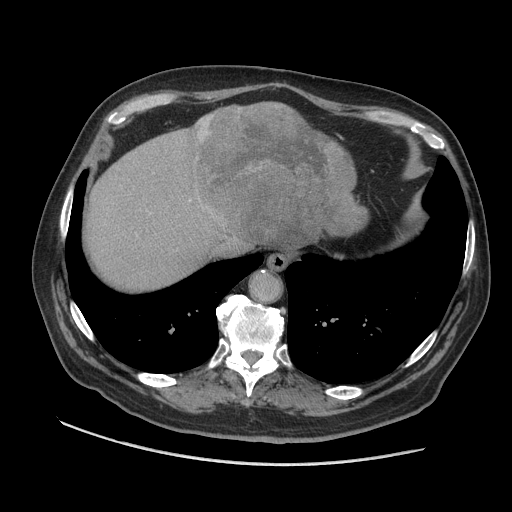
Contrast-enhanced abdominal CT (liver protocol), one axial slice; position 83 of 109 along the scan axis; reconstruction kernel STANDARD; 140 kVp; soft-tissue window (W 400 / L 40 HU); 2.5 mm slice thickness; 512 × 512 image matrix, field of view 420 × 420 mm. From the clinical record (not read from this slice): diagnosis: hepatocellular carcinoma (patient treated with transarterial chemoembolisation; whether this scan precedes or follows treatment is not stated here); TNM stage (as recorded): Stage-I; Child-Pugh class: A.
Outlined on this slice (semi-automatically segmented with operator editing):
- liver parenchyma outside the tumour (the mass and vessels are separate outlines, so this box may not span the whole liver): box from (x=84, y=102) to (x=302, y=290) px
- mass: (x=187, y=103)–(x=368, y=248)